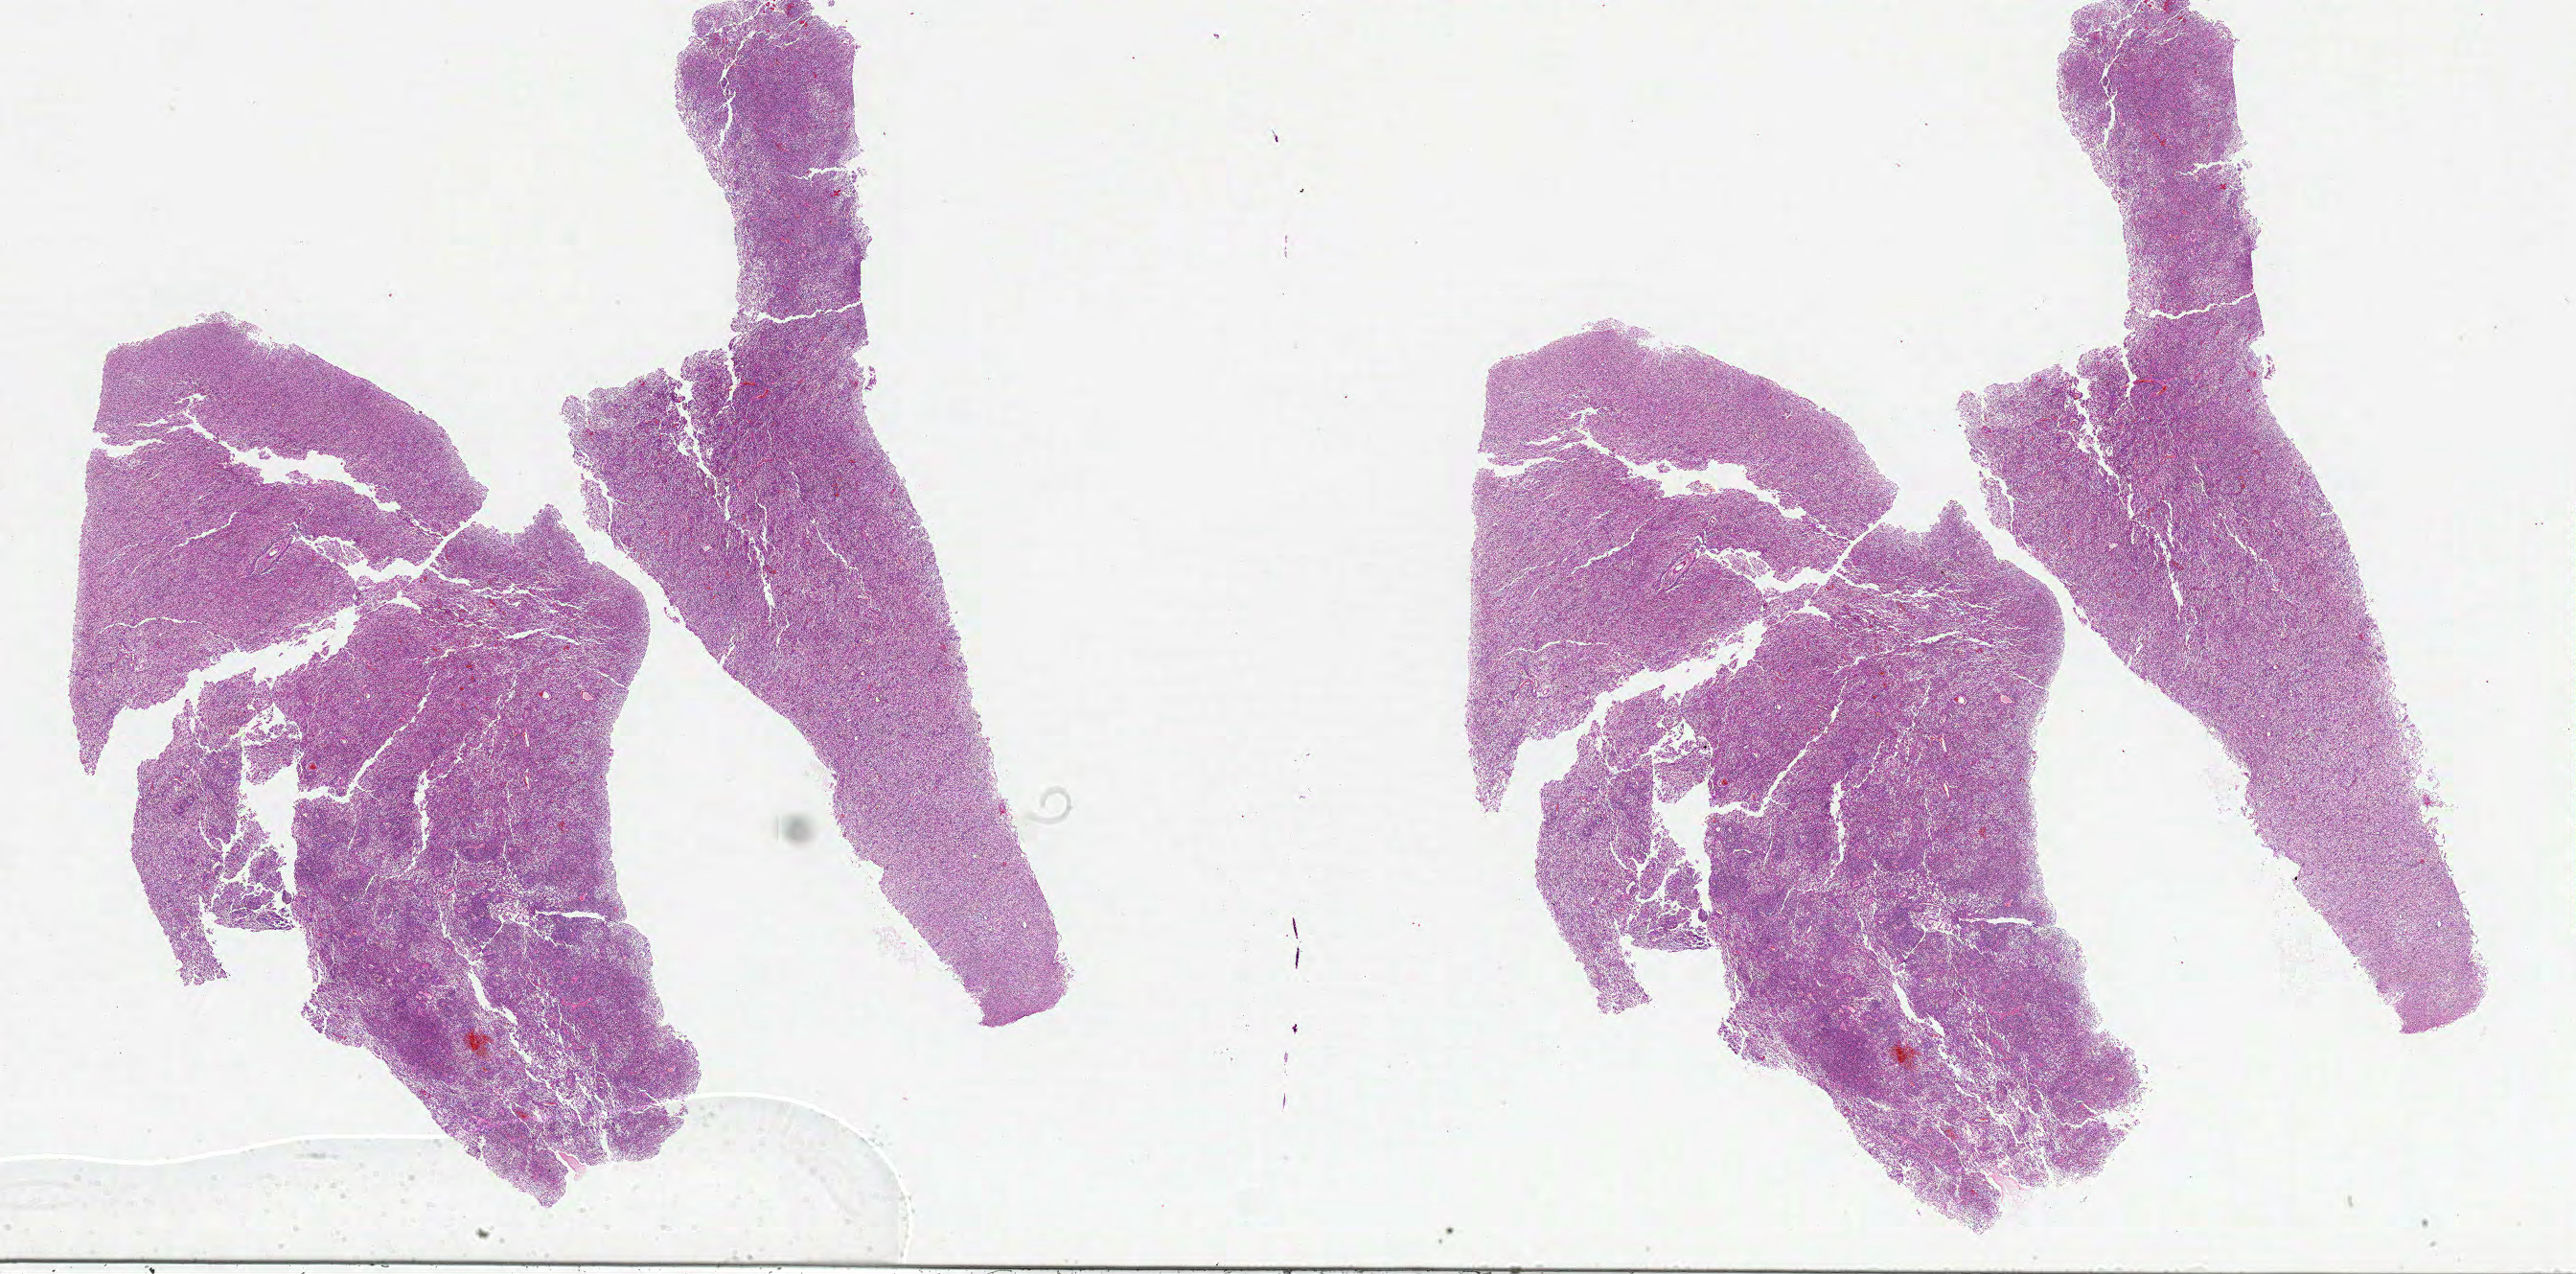
Whole-slide histology image, Hematoxylin and eosin (H&E) stained — shown as a low-resolution overview of the whole scanned area (about 43.0 x 21.2 mm, from a 20x scan); formalin-fixed paraffin-embedded (FFPE) diagnostic section; primary tumour sample from the brain. Female, age 75 years at initial diagnosis.
Pathologic diagnosis: Glioblastoma.